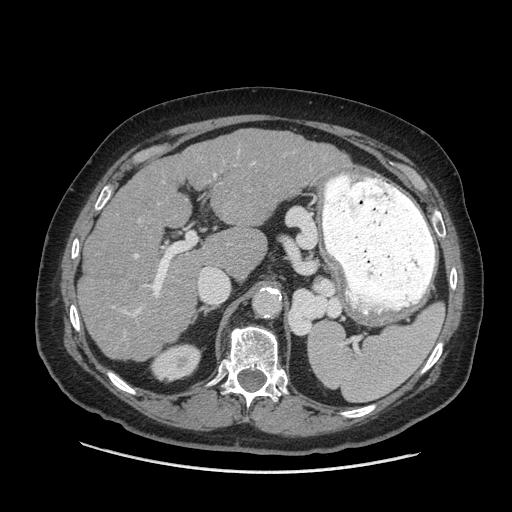
Contrast-enhanced abdominal CT (liver protocol), one axial slice; position 39 of 77 along the scan axis; reconstruction kernel STANDARD; 140 kVp; soft-tissue window (W 400 / L 40 HU); 512 × 512 image matrix, field of view 420 × 420 mm. Case-level facts recorded for this patient, not image findings: diagnosis: hepatocellular carcinoma (patient treated with transarterial chemoembolisation; whether this scan precedes or follows treatment is not stated here); TNM stage (as recorded): Stage-I; Child-Pugh class: A.
Annotated regions visible in this slice (semi-automatically segmented with operator editing):
- liver parenchyma outside the tumour (the mass and vessels are separate outlines, so this box may not span the whole liver): bounding box [x1, y1, x2, y2] px = [78, 128, 351, 360]
- liver vessels: [124, 162, 255, 317]